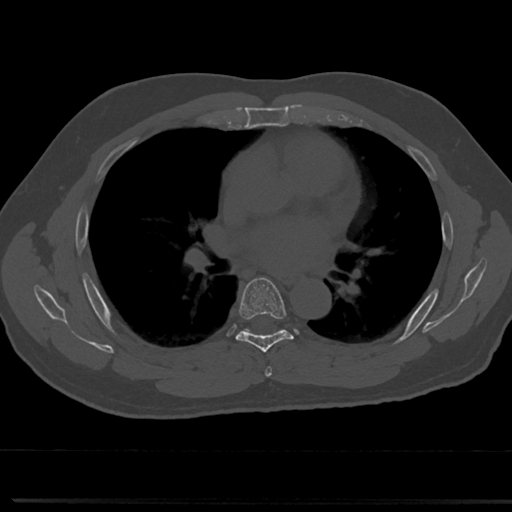
CT including the spine, one axial slice; reconstruction kernel Br40s/3; 120 kVp; bone window (W 1800 / L 400 HU); 0.5 mm slice thickness; 512 × 512 image matrix, field of view 355 × 355 mm. Male patient, age 61 years. From the clinical record (not read from this slice): primary cancer: prostate.
Annotated regions visible in this slice (semi-automatic segmentation, software-assisted and operator-edited):
- T5 vertebra: box from (x=264, y=349) to (x=273, y=376) px
- T6 vertebra: (x=218, y=277)–(x=311, y=354)